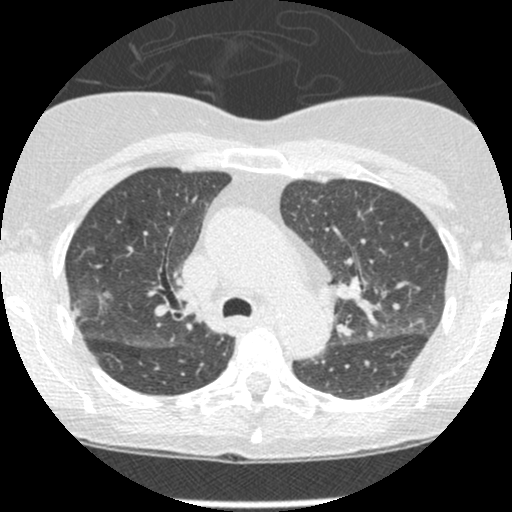
Low-dose screening chest CT, one axial slice. Slice 171 of 238 in the series (ordered by position). 120 kVp. Lung window (W 1500 / L -600 HU). 1.25 mm slice thickness. 512 × 512 image matrix, field of view 288 × 288 mm.
Structures marked on this image (manually delineated by an expert):
- lesion 1 (tumor, upper lobe of right lung): bounding box (x1, y1, x2, y2) in pixels: (98, 294, 108, 301)